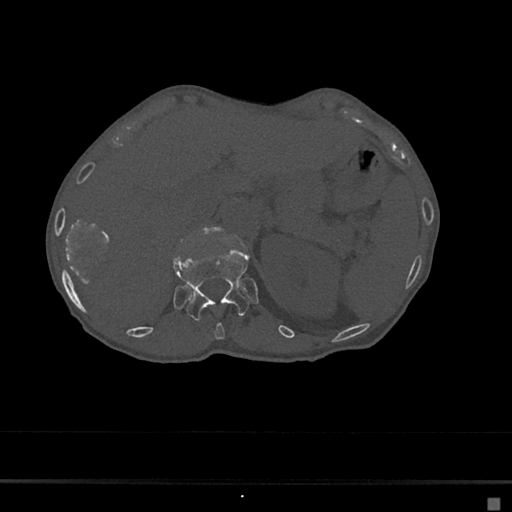
CT including the spine, one axial slice; position 127 of 797 along the scan axis; 120 kVp; bone window (W 1800 / L 400 HU); 0.5 mm slice thickness; 512 × 512 image matrix. Female patient, age 68 years. Case-level facts recorded for this patient, not image findings: primary cancer: renal.
Annotated regions visible in this slice (semi-automatically segmented with operator editing):
- T11 vertebra: bounding box [x1, y1, x2, y2] px = [215, 322, 225, 340]
- T12 vertebra: [173, 248, 249, 322]